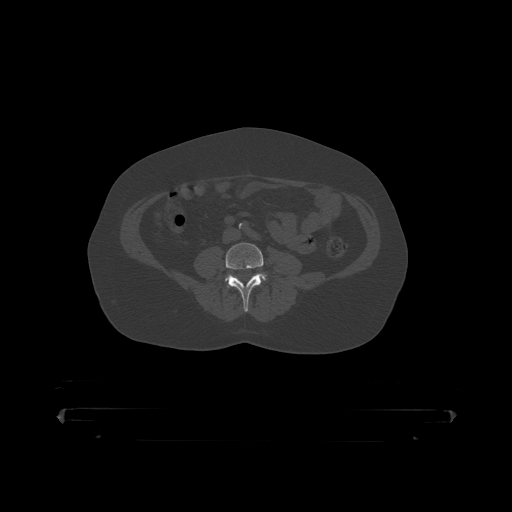
CT including the spine, one axial slice. Slice 61 of 390 in the series (ordered by position). Reconstruction kernel STANDARD. Bone window (W 1800 / L 400 HU). 512 × 512 image matrix, field of view 650 × 650 mm. Male patient, age 60 years. Case-level facts recorded for this patient, not image findings: primary cancer: prostate.
Structures marked on this image (semi-automatically segmented with operator editing):
- L4 vertebra: bounding box <226,243,268,313> (left, top, right, bottom; pixels)
- L5 vertebra: <227,274,266,282>